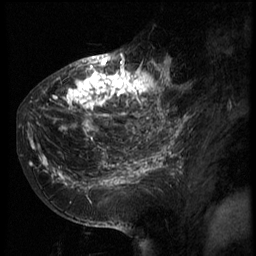
Breast MRI (dynamic contrast-enhanced), one sagittal slice; position 28 of 66 along the scan axis; 3 images stored at this slice position (order not interpretable as contrast timing); 1.5 T; TE 4.2 ms, TR 8.9 ms; 2.5 mm slice thickness; 256 × 256 image matrix, field of view 200 × 200 mm. Female patient, age 39 years. From the clinical record (not read from this slice): setting: breast cancer imaged before/during neoadjuvant chemotherapy; receptor status: HER2-positive.
Annotated regions visible in this slice (semi-automatically segmented with operator editing):
- analysis volume of interest (the breast-tissue region the enhancement analysis was run in; not a lesion): bounding box (x1, y1, x2, y2) in pixels: (29, 44, 166, 196)
- tumour enhancement mask (voxels above the 140 % enhancement threshold inside the analysis volume of interest): (29, 54, 166, 189)